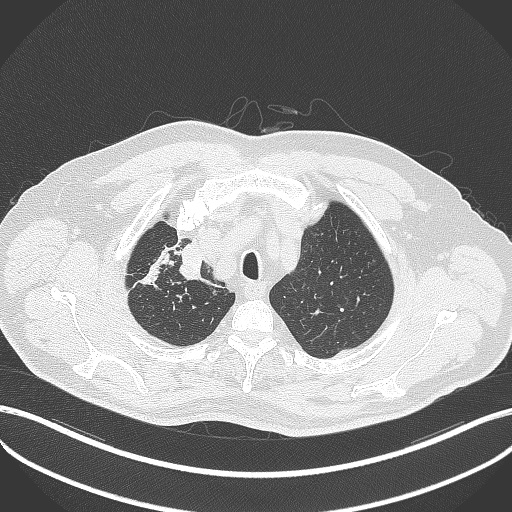
Chest CT, one axial slice; position 328 of 411 along the scan axis; 120 kVp; lung window (W 1500 / L -600 HU); 1 mm slice thickness; 512 × 512 image matrix, field of view 400 × 400 mm. Male patient, age 60 years. From the clinical record (not read from this slice): clinical TNM (as recorded): T1b N1 M0.
Outlined on this slice (bounding box drawn by a radiologist):
- lung tumour (recorded histology: squamous cell carcinoma): bounding box [x1, y1, x2, y2] px = [178, 239, 227, 296]